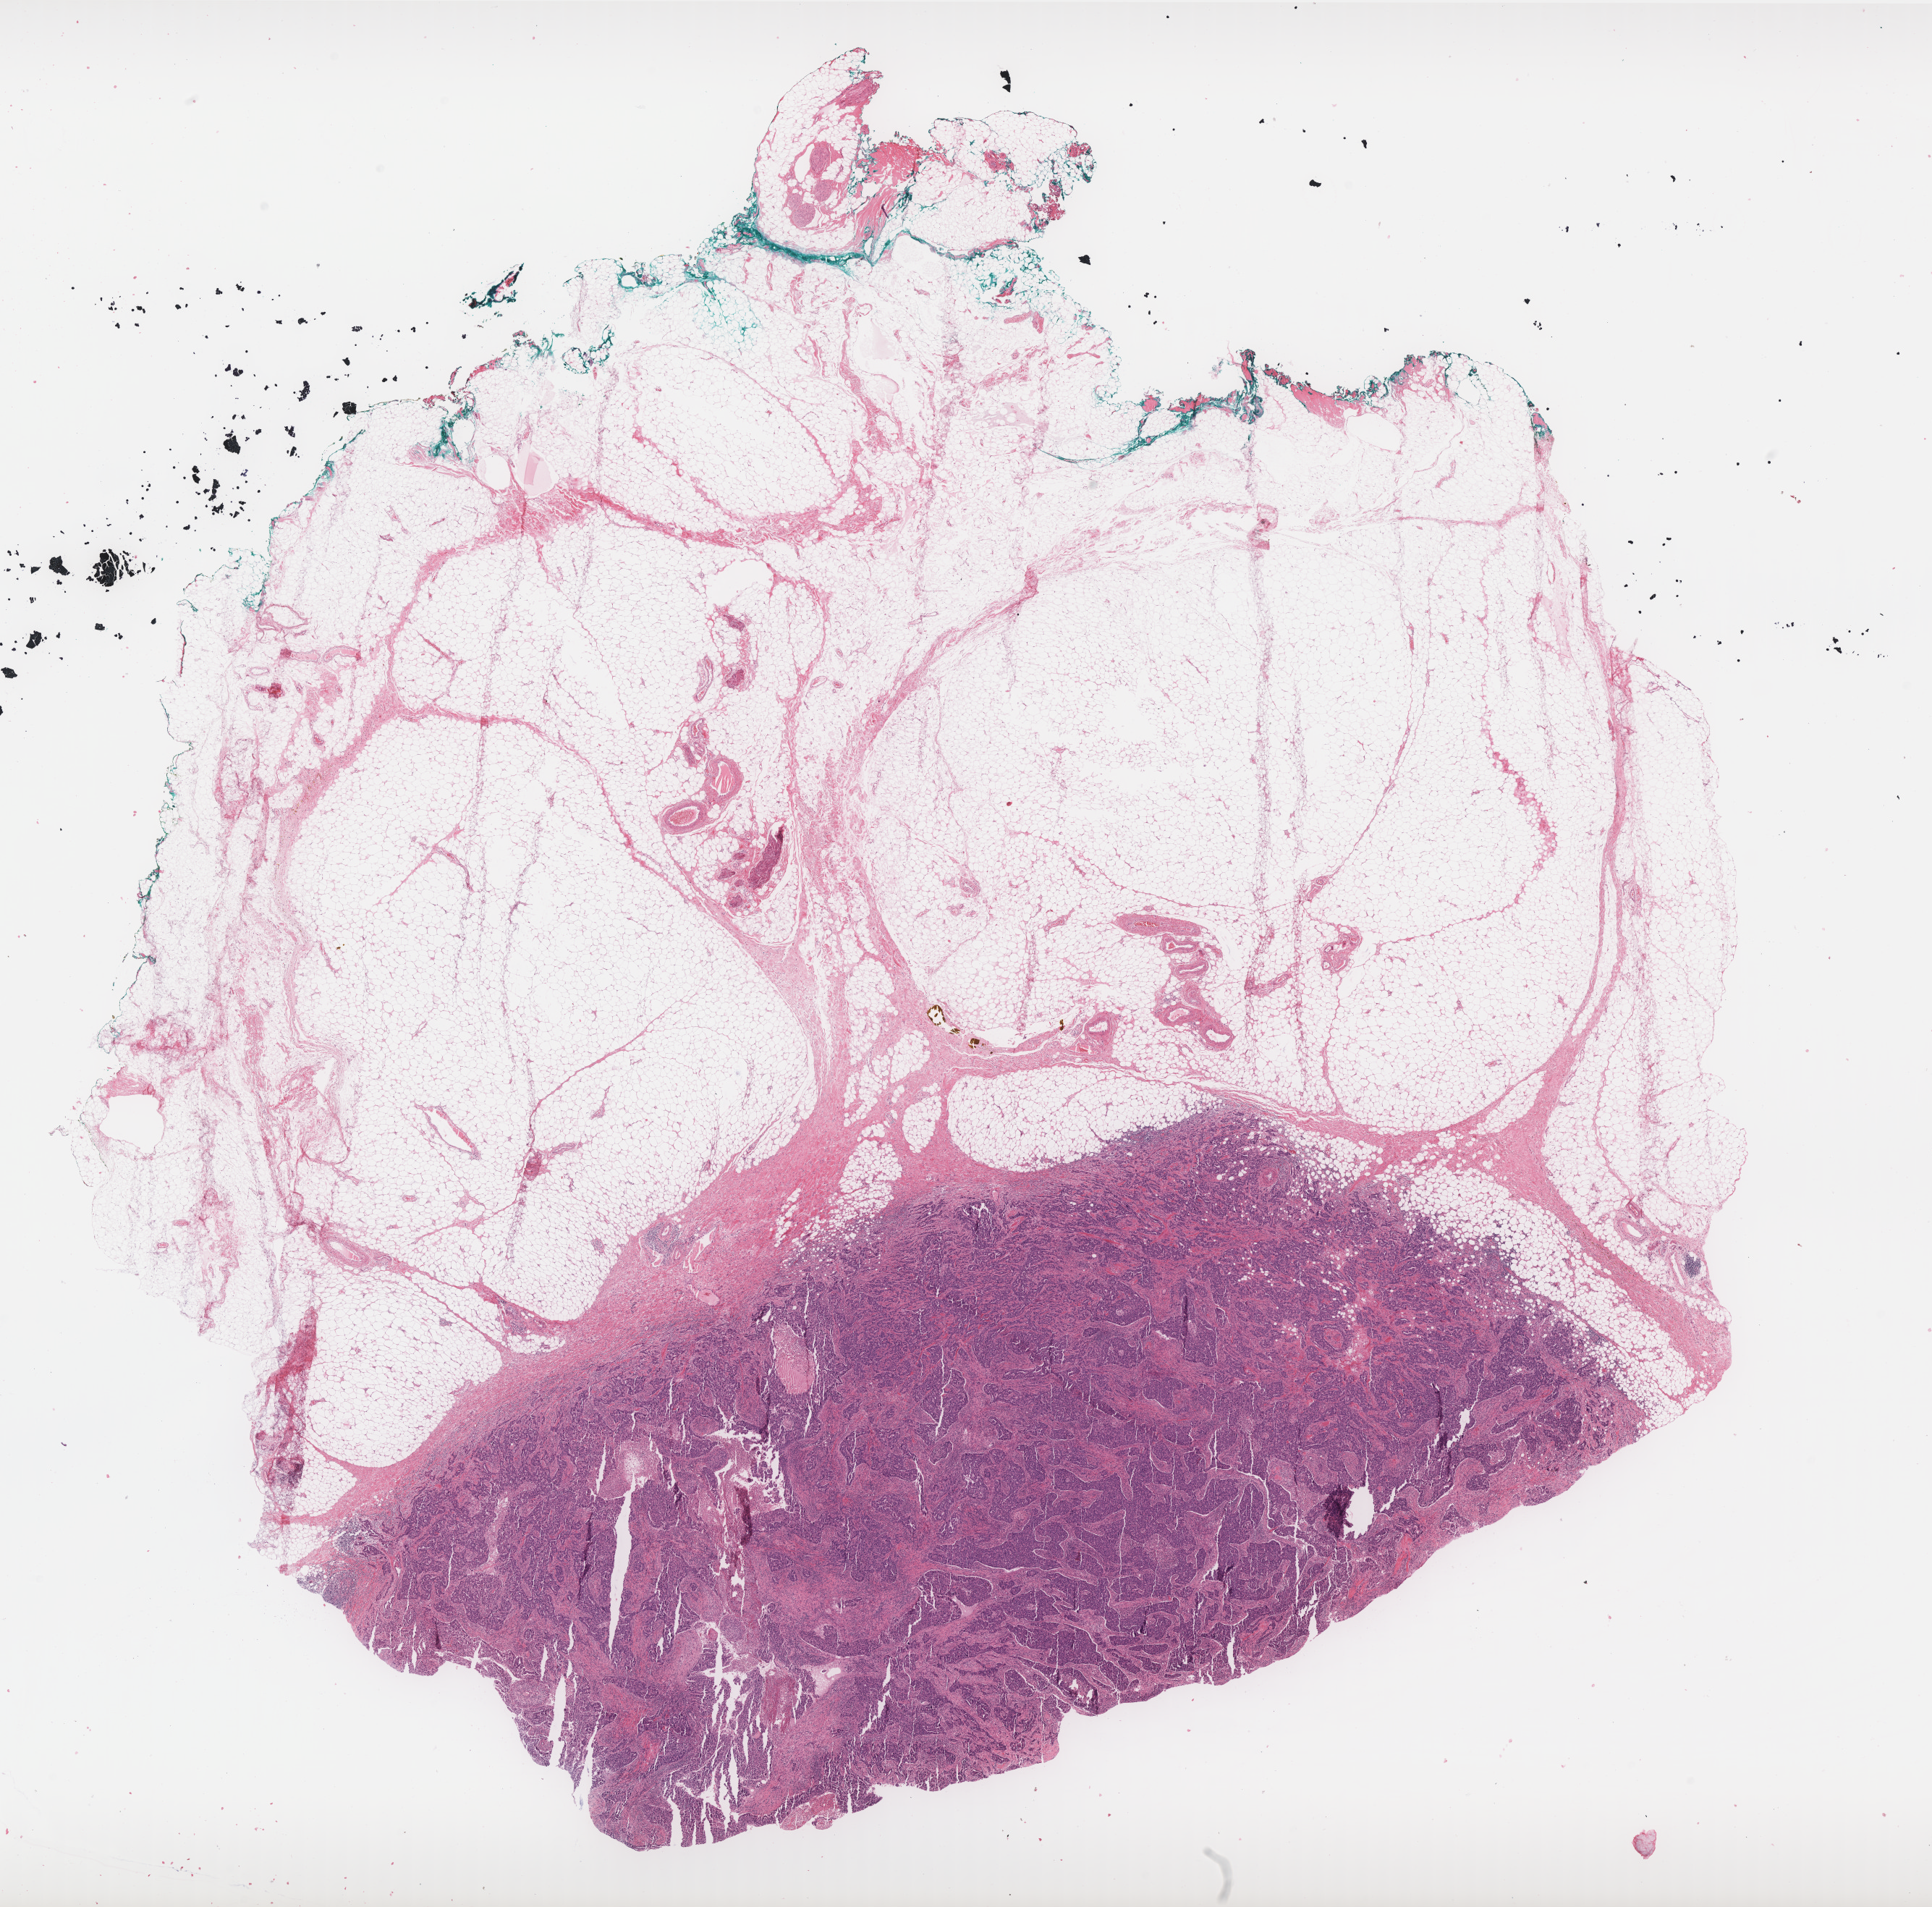
Whole-slide histology image, Hematoxylin and eosin (H&E) stained, shown as a low-resolution overview of the whole scanned area (about 21.4 x 21.1 mm, slide scanned at 40x), FFPE section, sample: primary tumour, breast. Female patient; age at initial diagnosis 67 years.
• AJCC pathologic stage: IIA
• lymph nodes positive (case pathology): 0 of 5 examined
• pathologic diagnosis: Infiltrating duct carcinoma, NOS